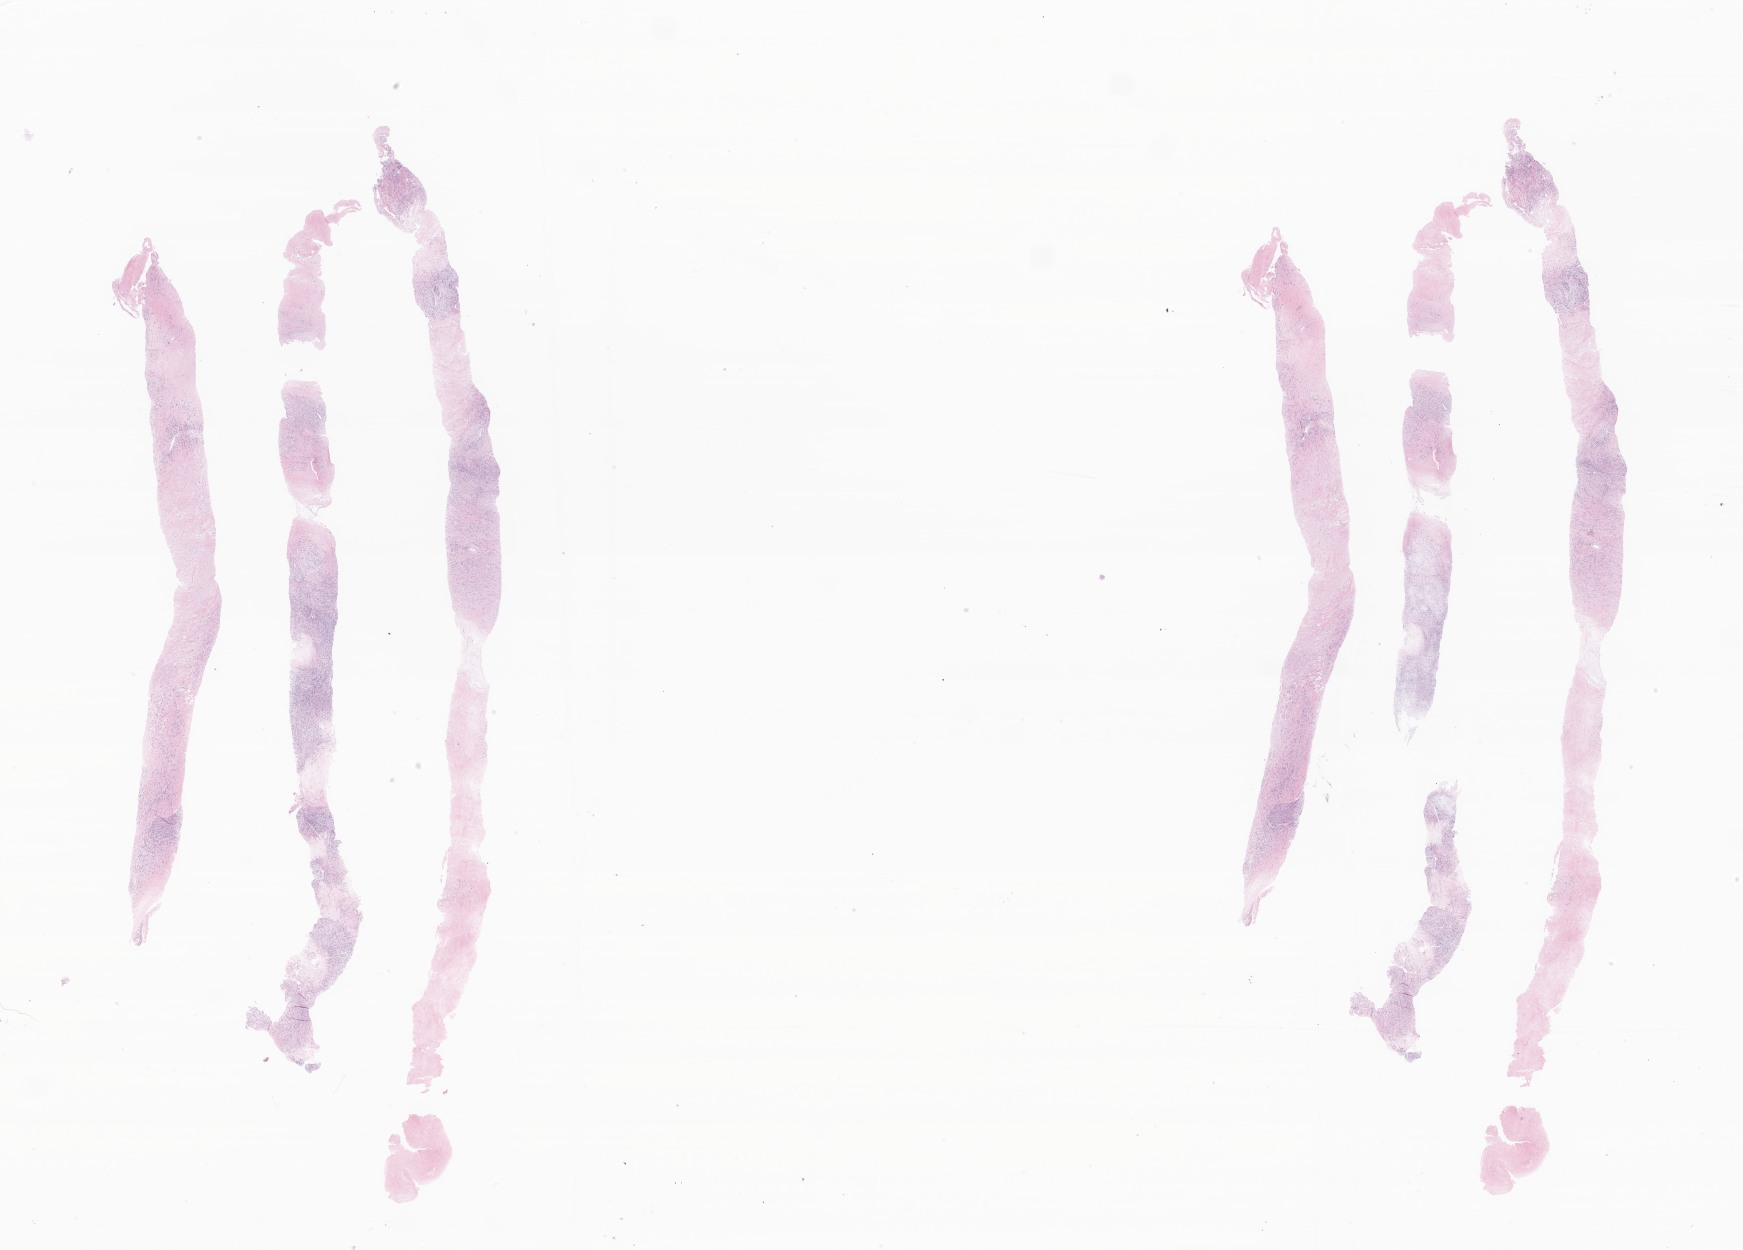
Hematoxylin and eosin (H&E) whole-slide image of tumor tissue from the soft tissue of lower extremity, whole scanned area (about 29.4 x 21.1 mm) shown as a low-resolution overview. Formalin-fixed paraffin-embedded section. Patient: female, age 269 months (22 years 5 months).
Diagnosis: Malignant peripheral nerve sheath tumor, NOS.